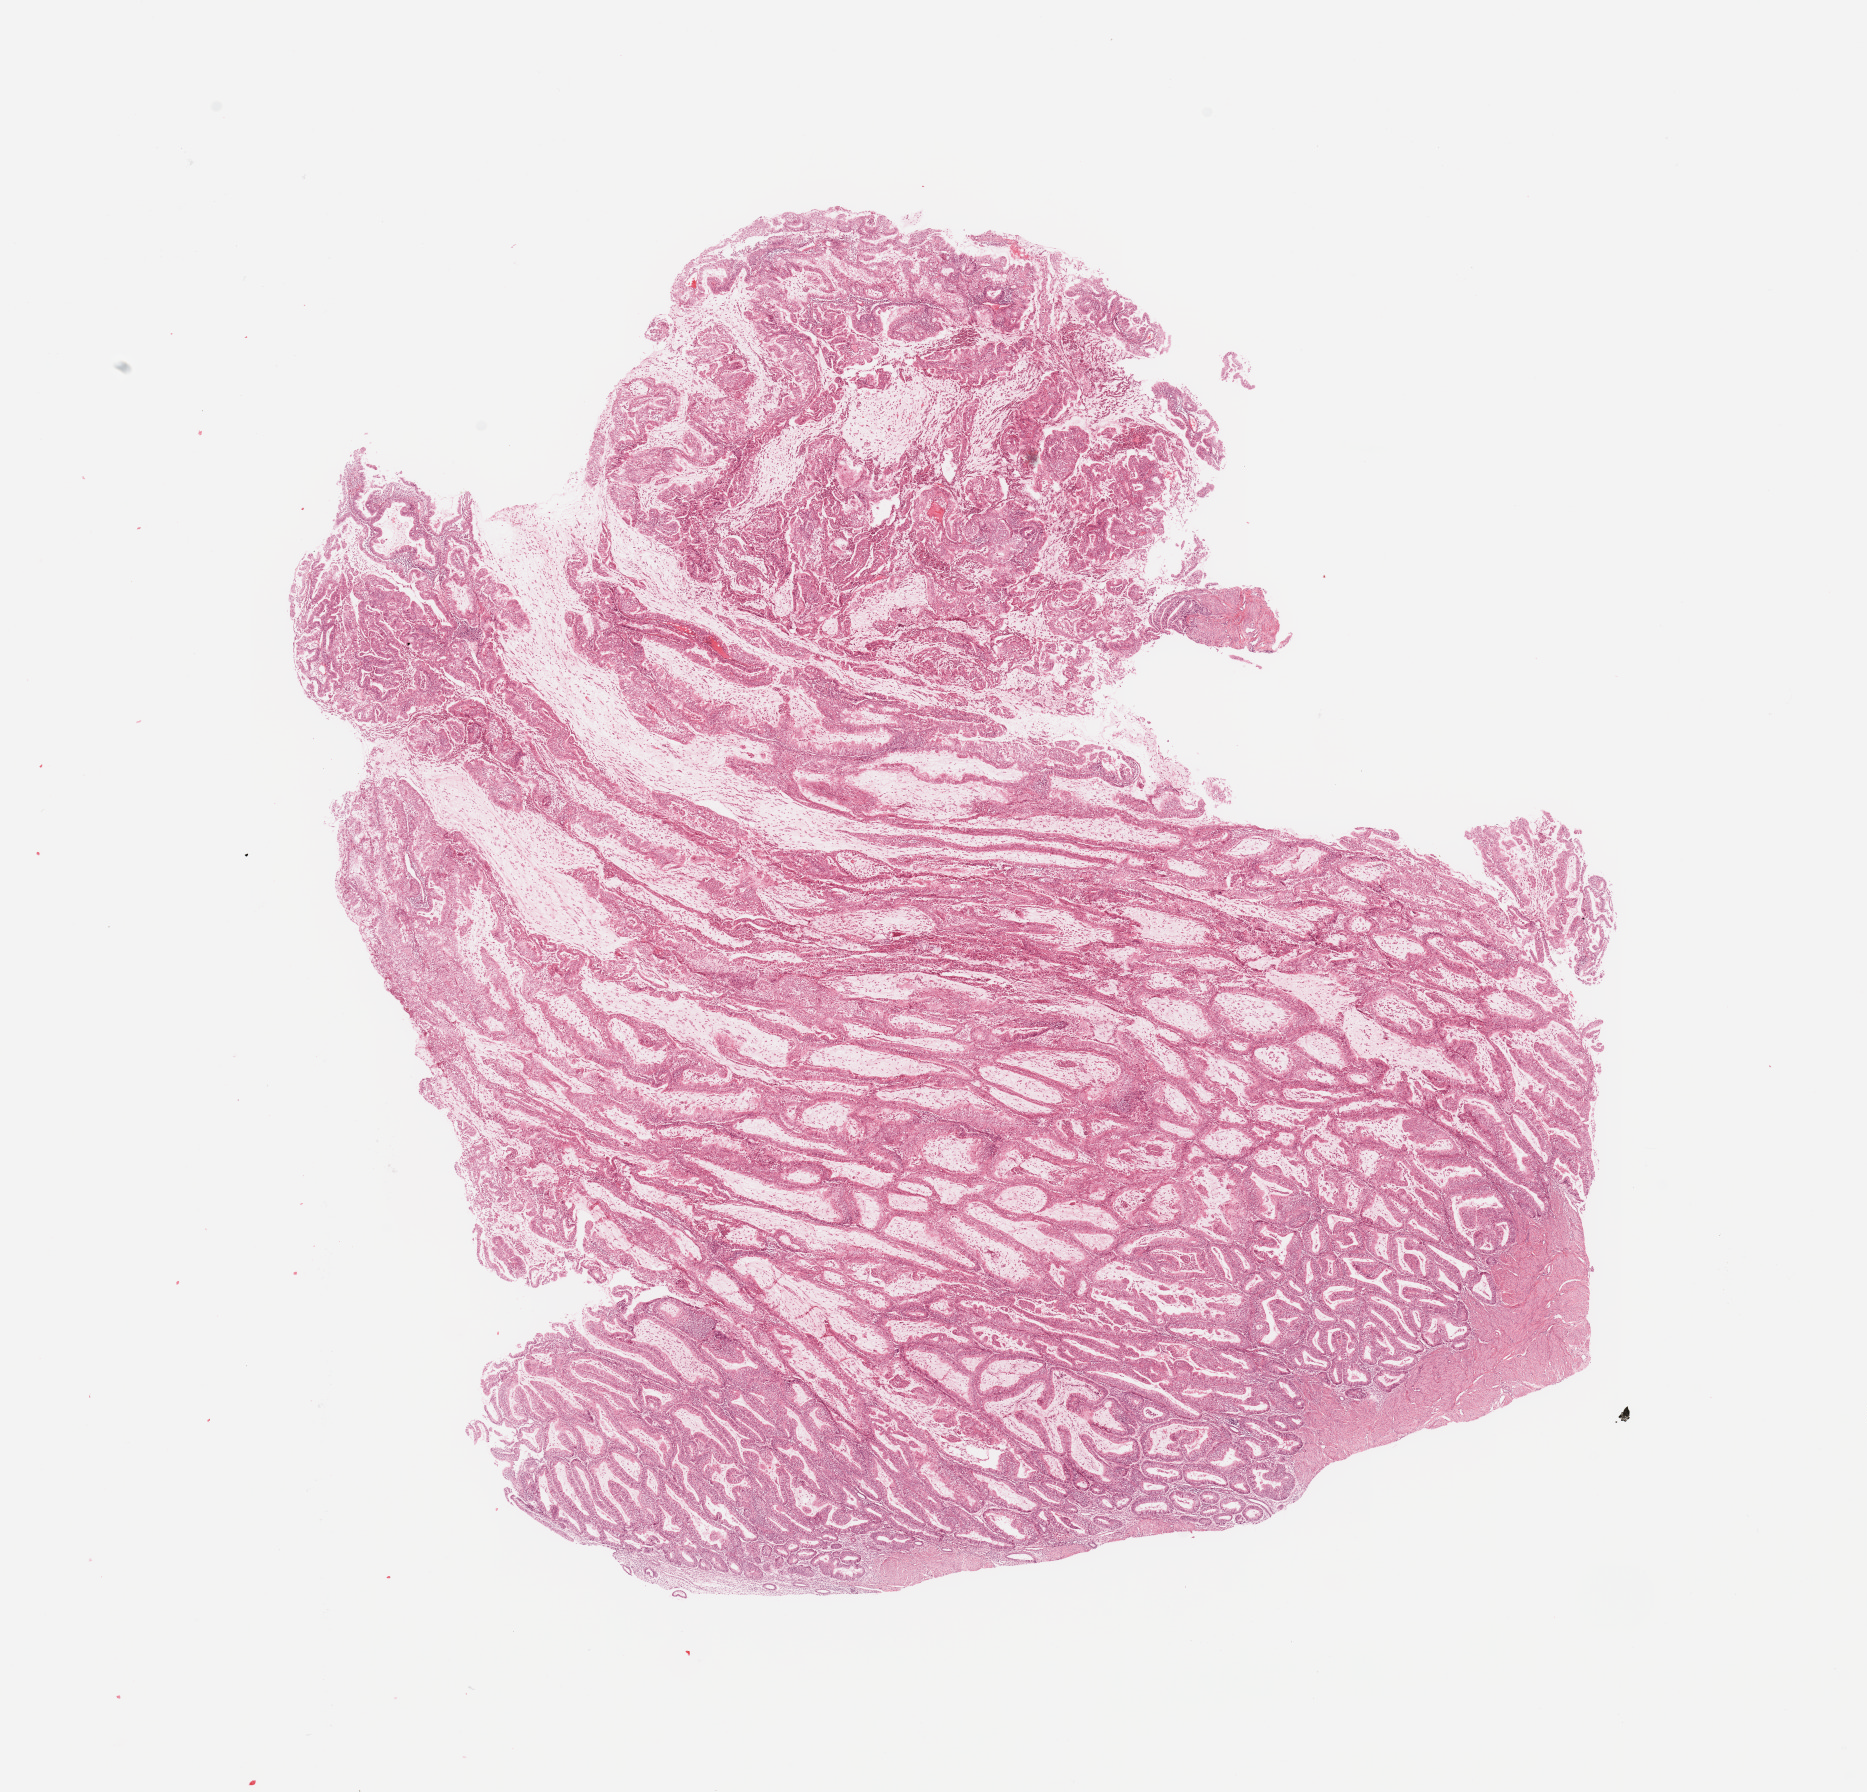
Digitized H&E tissue section (whole slide), low-resolution overview of the scanned area, about 14.8 x 14.2 mm; uterus, tumour tissue. Patient: female, age 57 years. Histologic grade: G1 (well differentiated).
AJCC pathologic stage: I. Histologic diagnosis: Endometrioid adenocarcinoma, NOS.